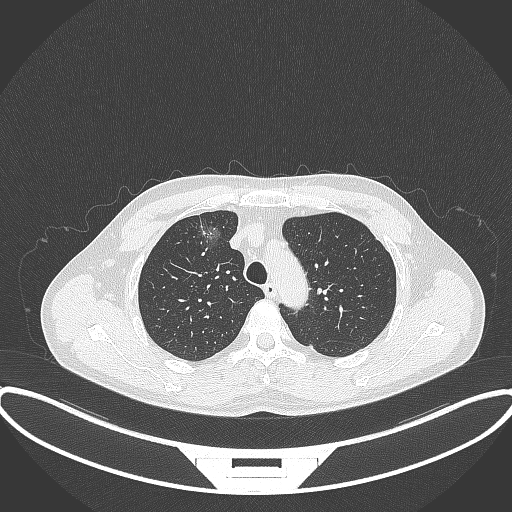
Chest CT, one axial slice; position 280 of 395 along the scan axis; reconstruction kernel B70f; lung window (W 1500 / L -600 HU); 512 × 512 image matrix, field of view 424 × 424 mm. Male patient, age 60 years. From the clinical record (not read from this slice): clinical TNM (as recorded): T1c N0 M0.
Outlined on this slice (rectangle marked by the reading radiologist):
- lung tumour (recorded histology: adenocarcinoma): bounding box <195,221,223,255> (left, top, right, bottom; pixels)